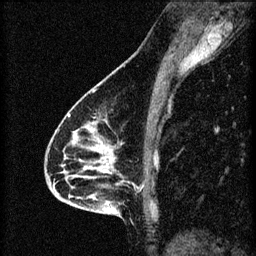
Breast MRI (dynamic contrast-enhanced), one sagittal slice; 3 images stored at this slice position (order not interpretable as contrast timing); 1.5 T; TE 4.2 ms, TR 8.2 ms; 2 mm slice thickness; 256 × 256 image matrix, field of view 180 × 180 mm. Female patient, age 46 years.
Annotated regions visible in this slice (semi-automatically segmented with operator editing):
- analysis volume of interest (the breast-tissue region the enhancement analysis was run in; not a lesion): bounding box <55,114,148,209> (left, top, right, bottom; pixels)
- tumour enhancement mask (voxels above the 70 % enhancement threshold inside the analysis volume of interest): <68,114,113,173>